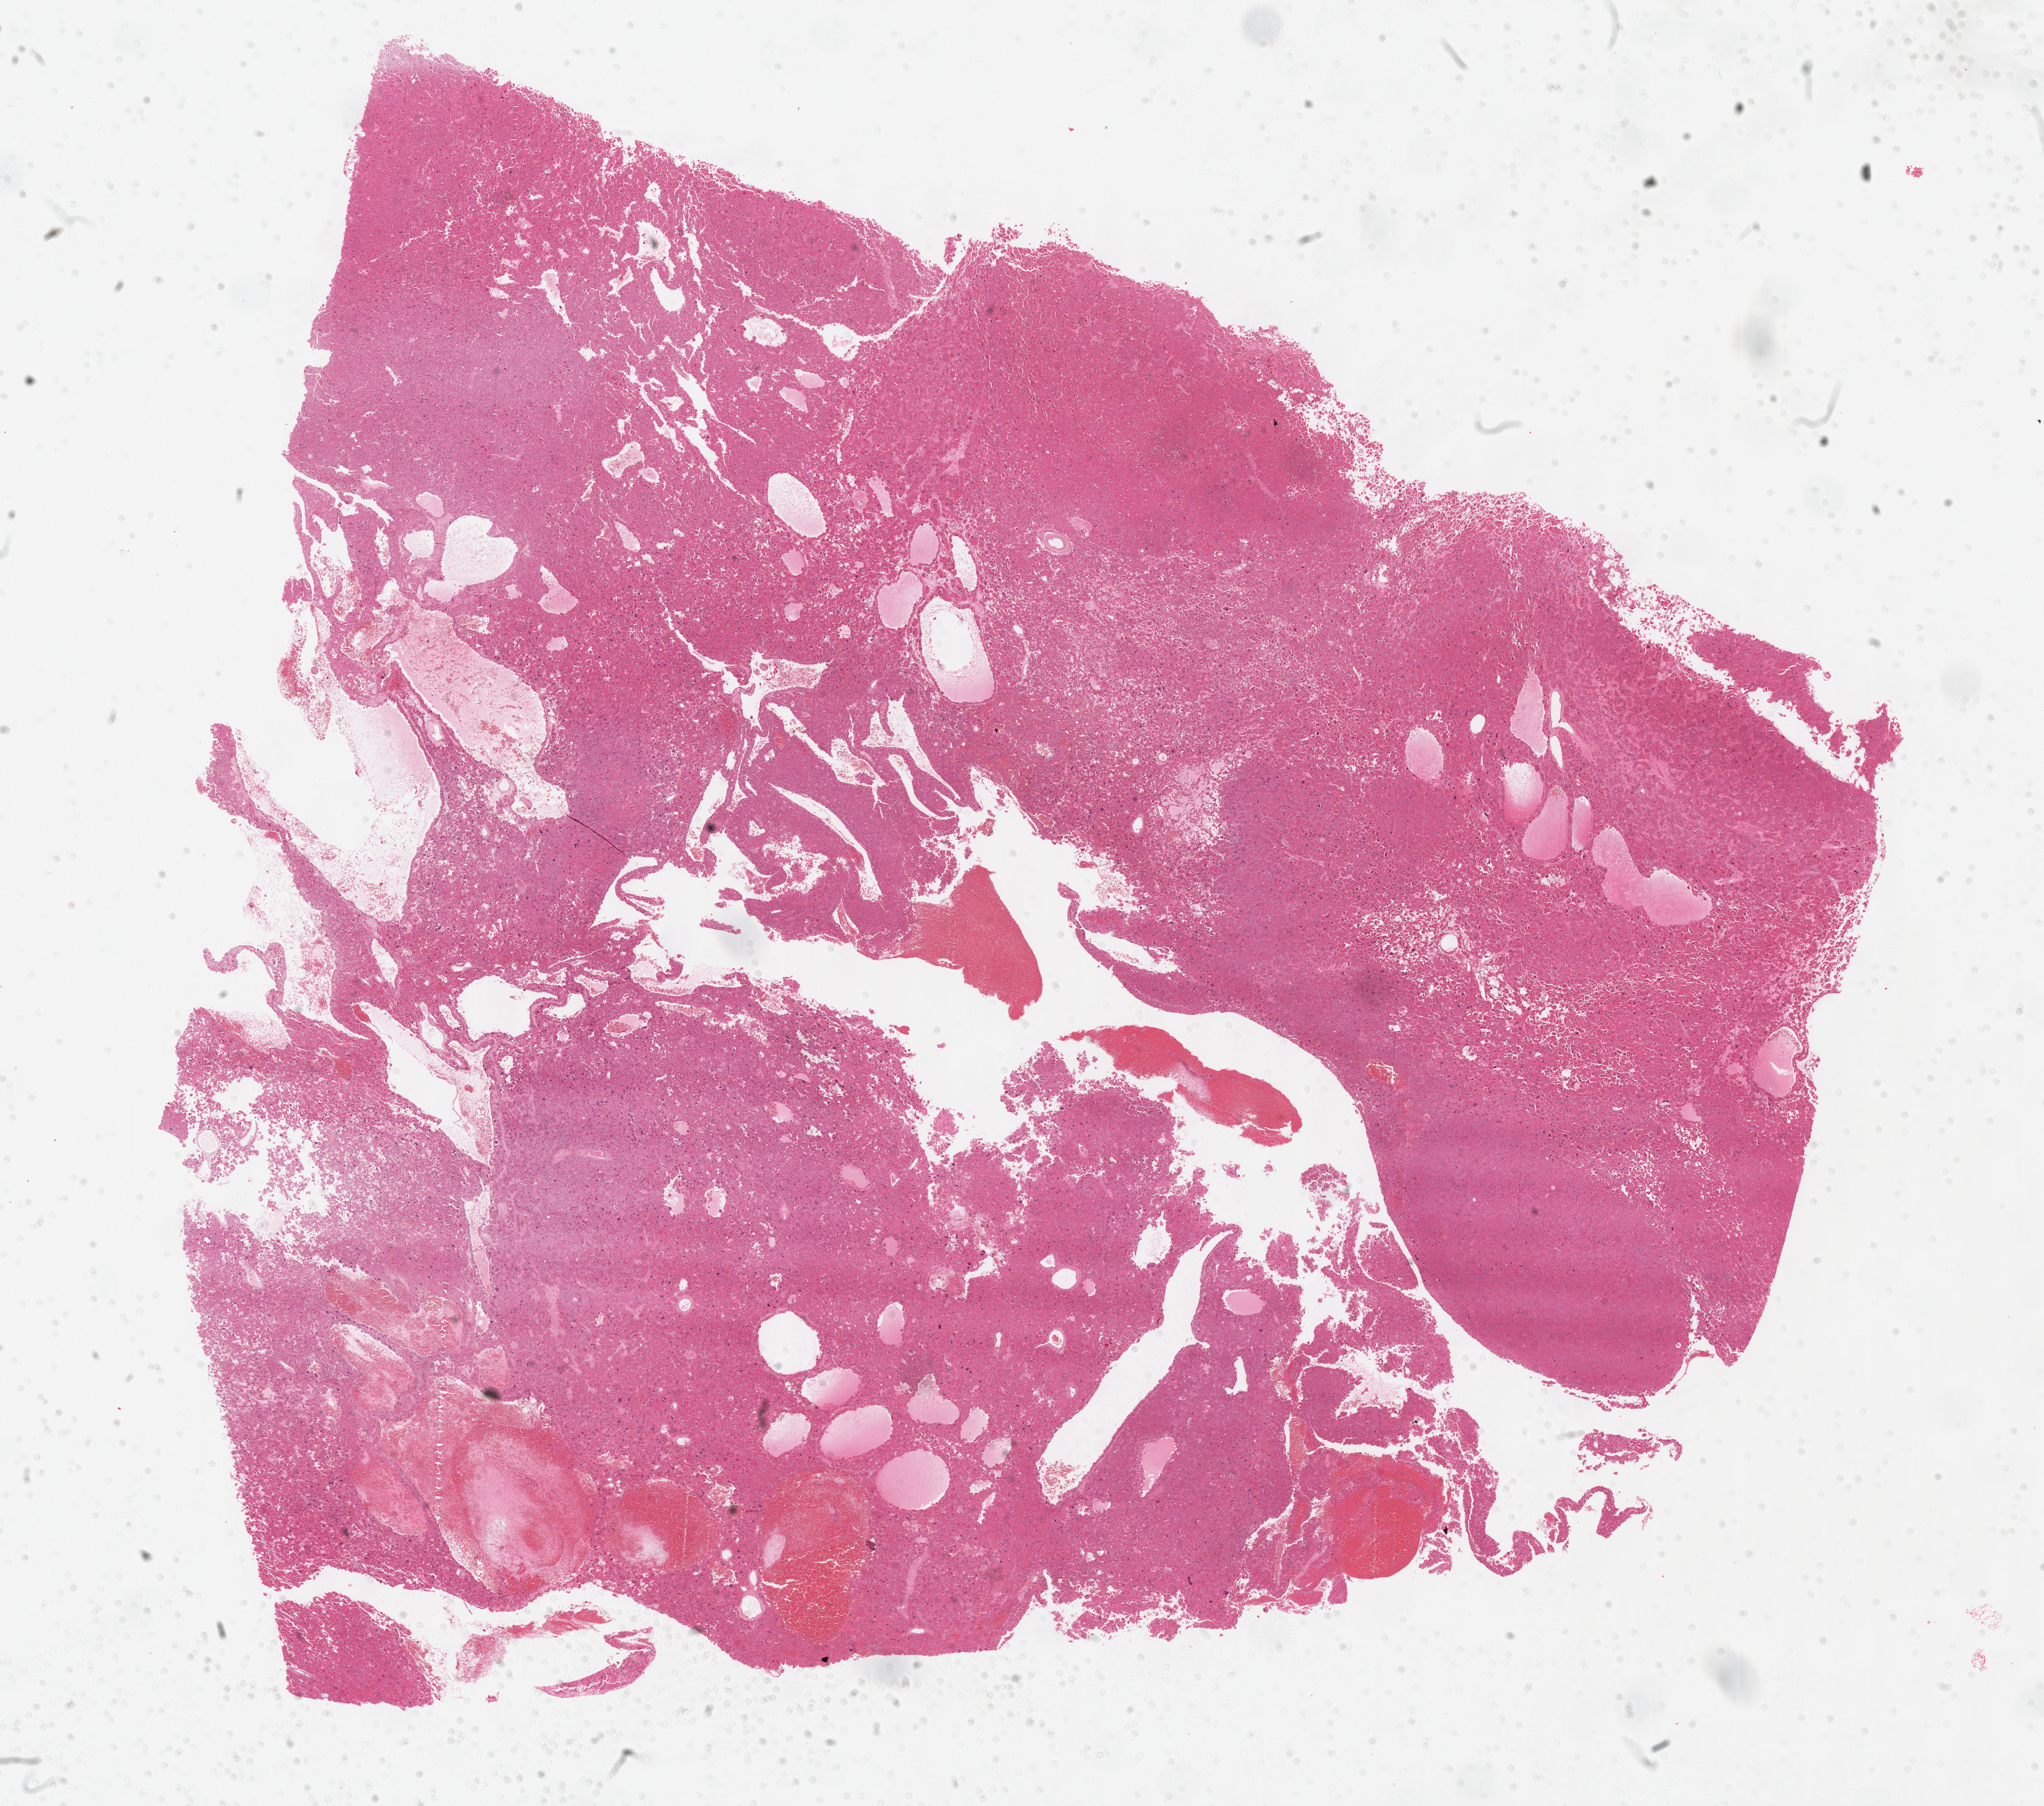
Whole-slide histology image, H&E, low-resolution overview of the scanned area, about 23.7 x 20.9 mm. Formalin-fixed paraffin-embedded (FFPE) diagnostic section. Primary tumour sample from the adrenal cortex. Female patient; age at initial diagnosis 57 years.
• laterality: left
• pathologic diagnosis: Adrenal cortical carcinoma